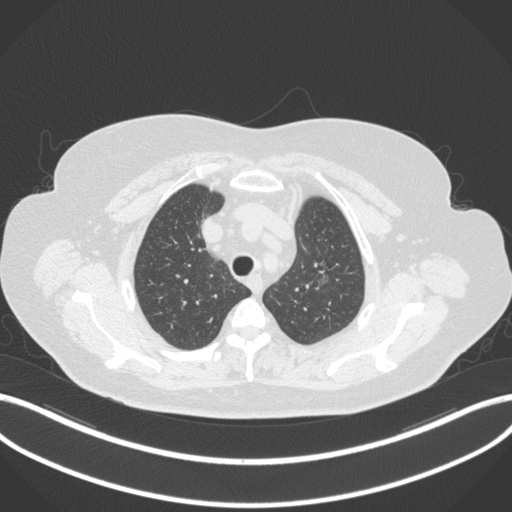
Chest CT, one axial slice. Position 274 of 310 along the scan axis. 120 kVp. Lung window (W 1500 / L -600 HU). 1 mm slice thickness. 512 × 512 image matrix, field of view 400 × 400 mm. Patient: female, 70 years. Case-level facts recorded for this patient, not image findings: clinical TNM (as recorded): T1c N0 M0.
Annotated regions visible in this slice (rectangle marked by the reading radiologist):
- lung tumour (recorded histology: adenocarcinoma): bounding box (x1, y1, x2, y2) in pixels: (313, 260, 329, 296)